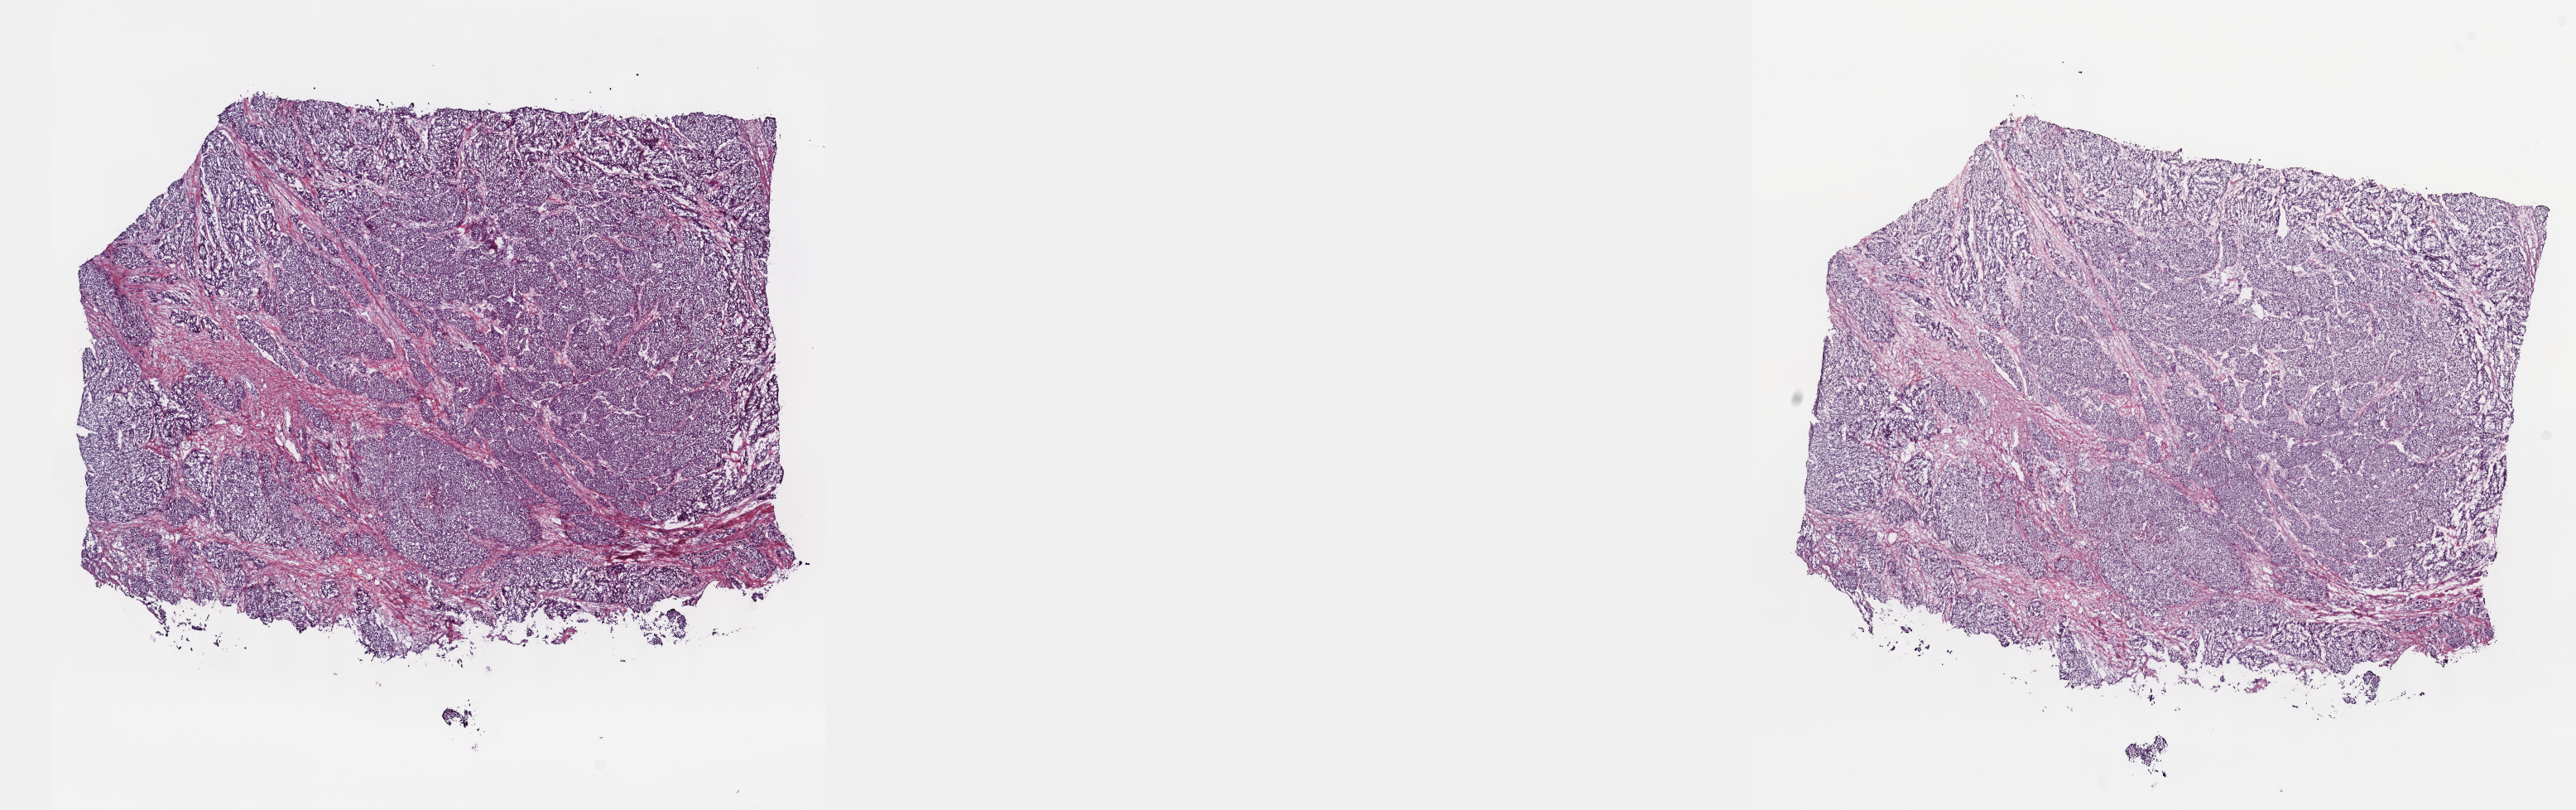
Digitized H&E-stained tissue section (whole slide), whole scanned area (about 25.1 x 7.9 mm, from a 40x scan) shown as a low-resolution overview. Frozen section from the top of the tissue portion. Bladder, primary tumour sample. Patient: female, age at initial diagnosis 87 years. Histologic grade: high grade. Slide review estimates, as recorded: tumour cells 75%, tumour nuclei 80%, normal cells 0%, stromal cells 25%, necrosis 0%. Infiltration values recorded for this section: lymphocyte infiltration 0%, monocyte infiltration 0%, neutrophil infiltration 0%.
• pathologic diagnosis: Transitional cell carcinoma
• AJCC pathologic stage: III (6th edition)
• lymph nodes positive (case pathology): 0 of 26 examined